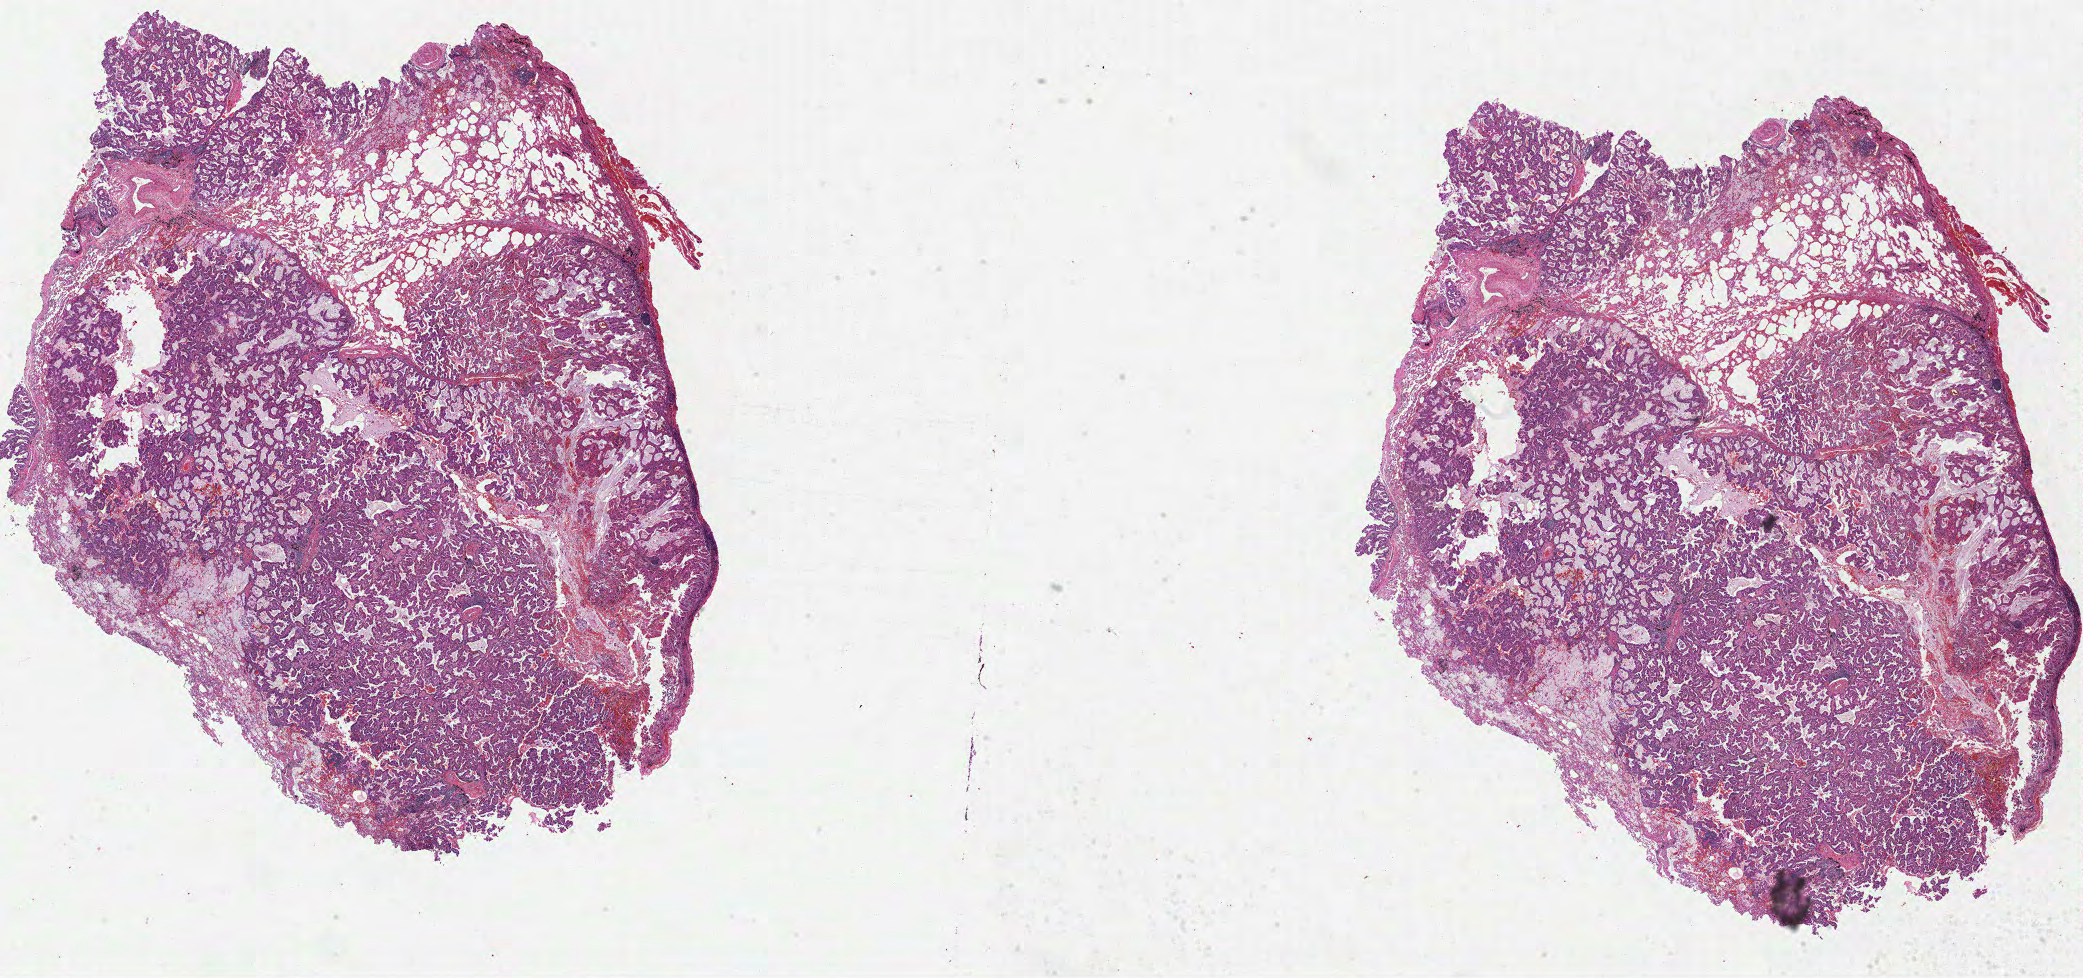
Whole-slide histology image, H&E-stained, low-resolution overview of the scanned area, about 33.6 x 15.8 mm; formalin-fixed paraffin-embedded (FFPE) diagnostic section; sample: primary tumour, lung. Male patient; age at initial diagnosis 57 years.
AJCC pathologic stage: IB. Laterality: right. Histologic diagnosis: Adenocarcinoma, NOS (upper lobe, lung).